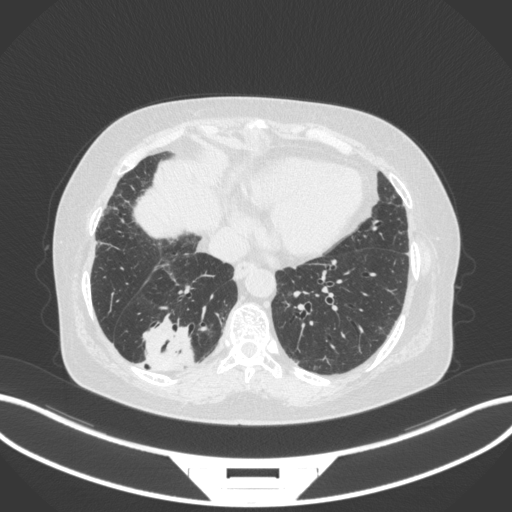
Chest CT, one axial slice. Position 61 of 303 along the scan axis. Reconstruction kernel B31f. 120 kVp. Lung window (W 1500 / L -600 HU). 1 mm slice thickness. 512 × 512 image matrix. Female patient, age 65 years. From the clinical record (not read from this slice): clinical TNM (as recorded): T2b N1 M0.
Structures marked on this image (rectangle marked by the reading radiologist):
- lung tumour (recorded histology: adenocarcinoma): bounding box <137,310,197,373> (left, top, right, bottom; pixels)